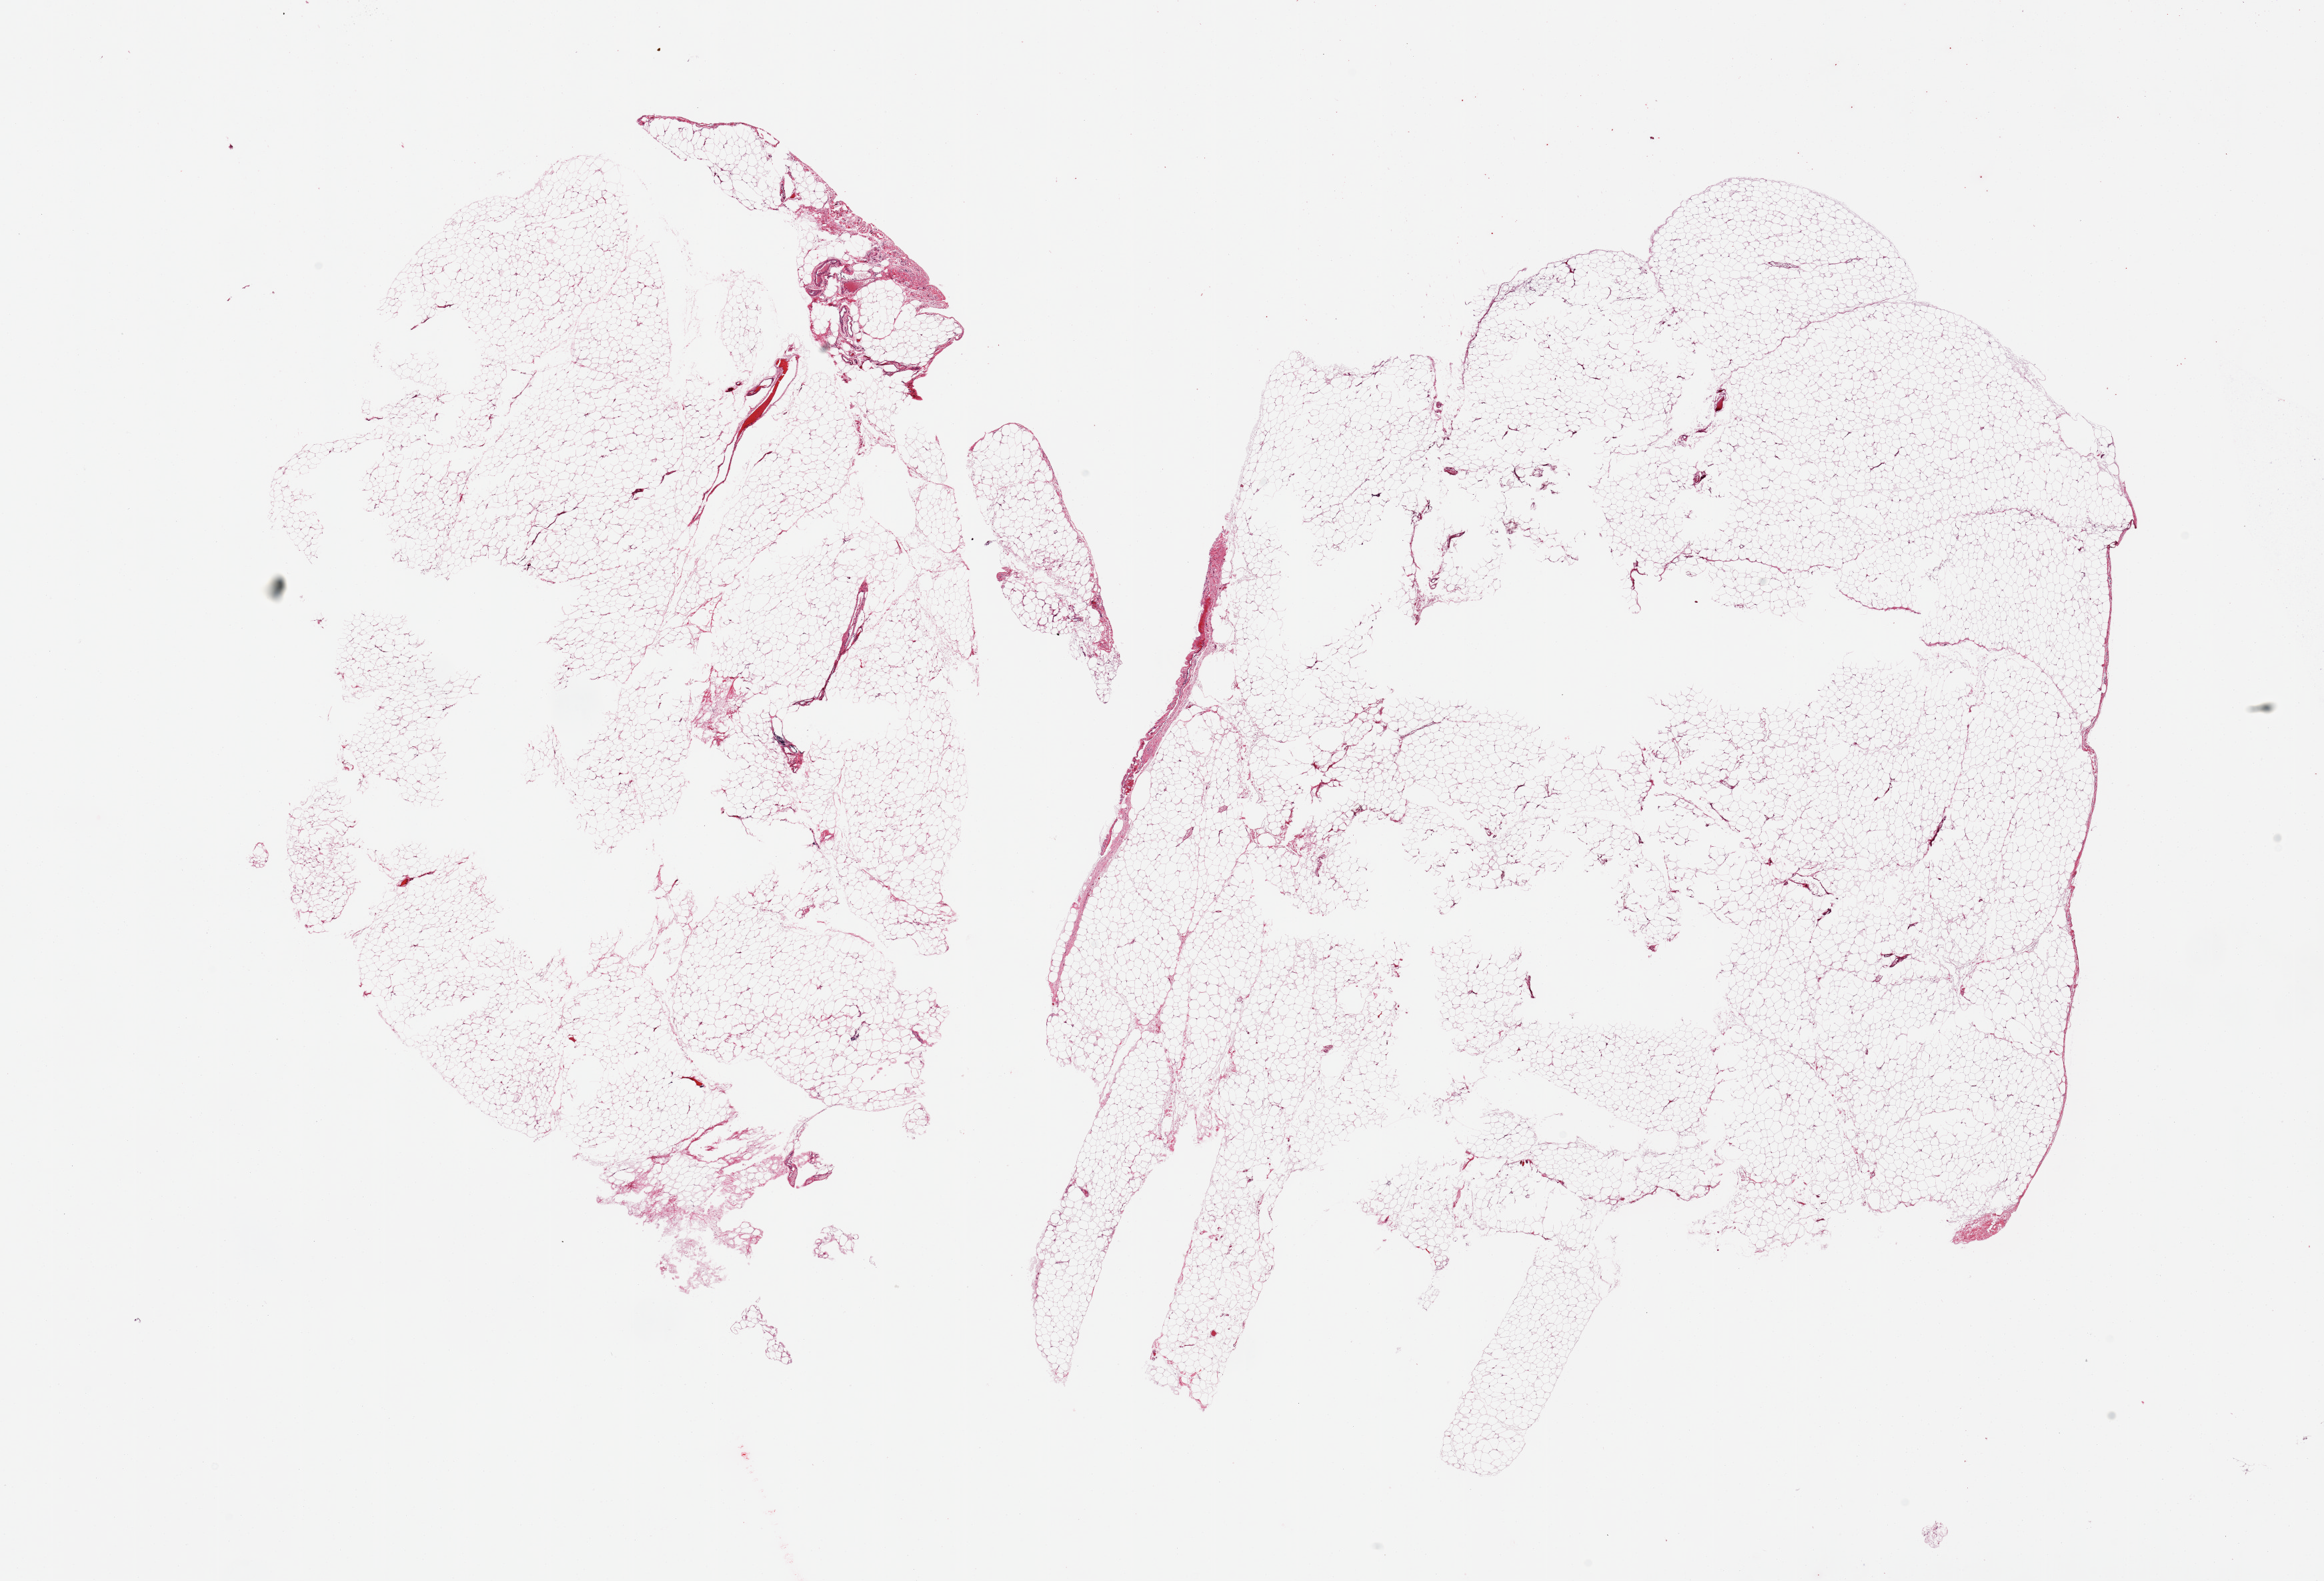
Hematoxylin and eosin (H&E) whole-slide image, whole scanned area (about 27.6 x 18.8 mm) shown as a low-resolution overview. PAXgene-fixed paraffin-embedded (PFPE) section. Sampled site (target tissue): omentum. Tissue donor sample. Donor: female.
Pathologist's review note for this sample: 2 pieces, minimal vascular elements/fascia.